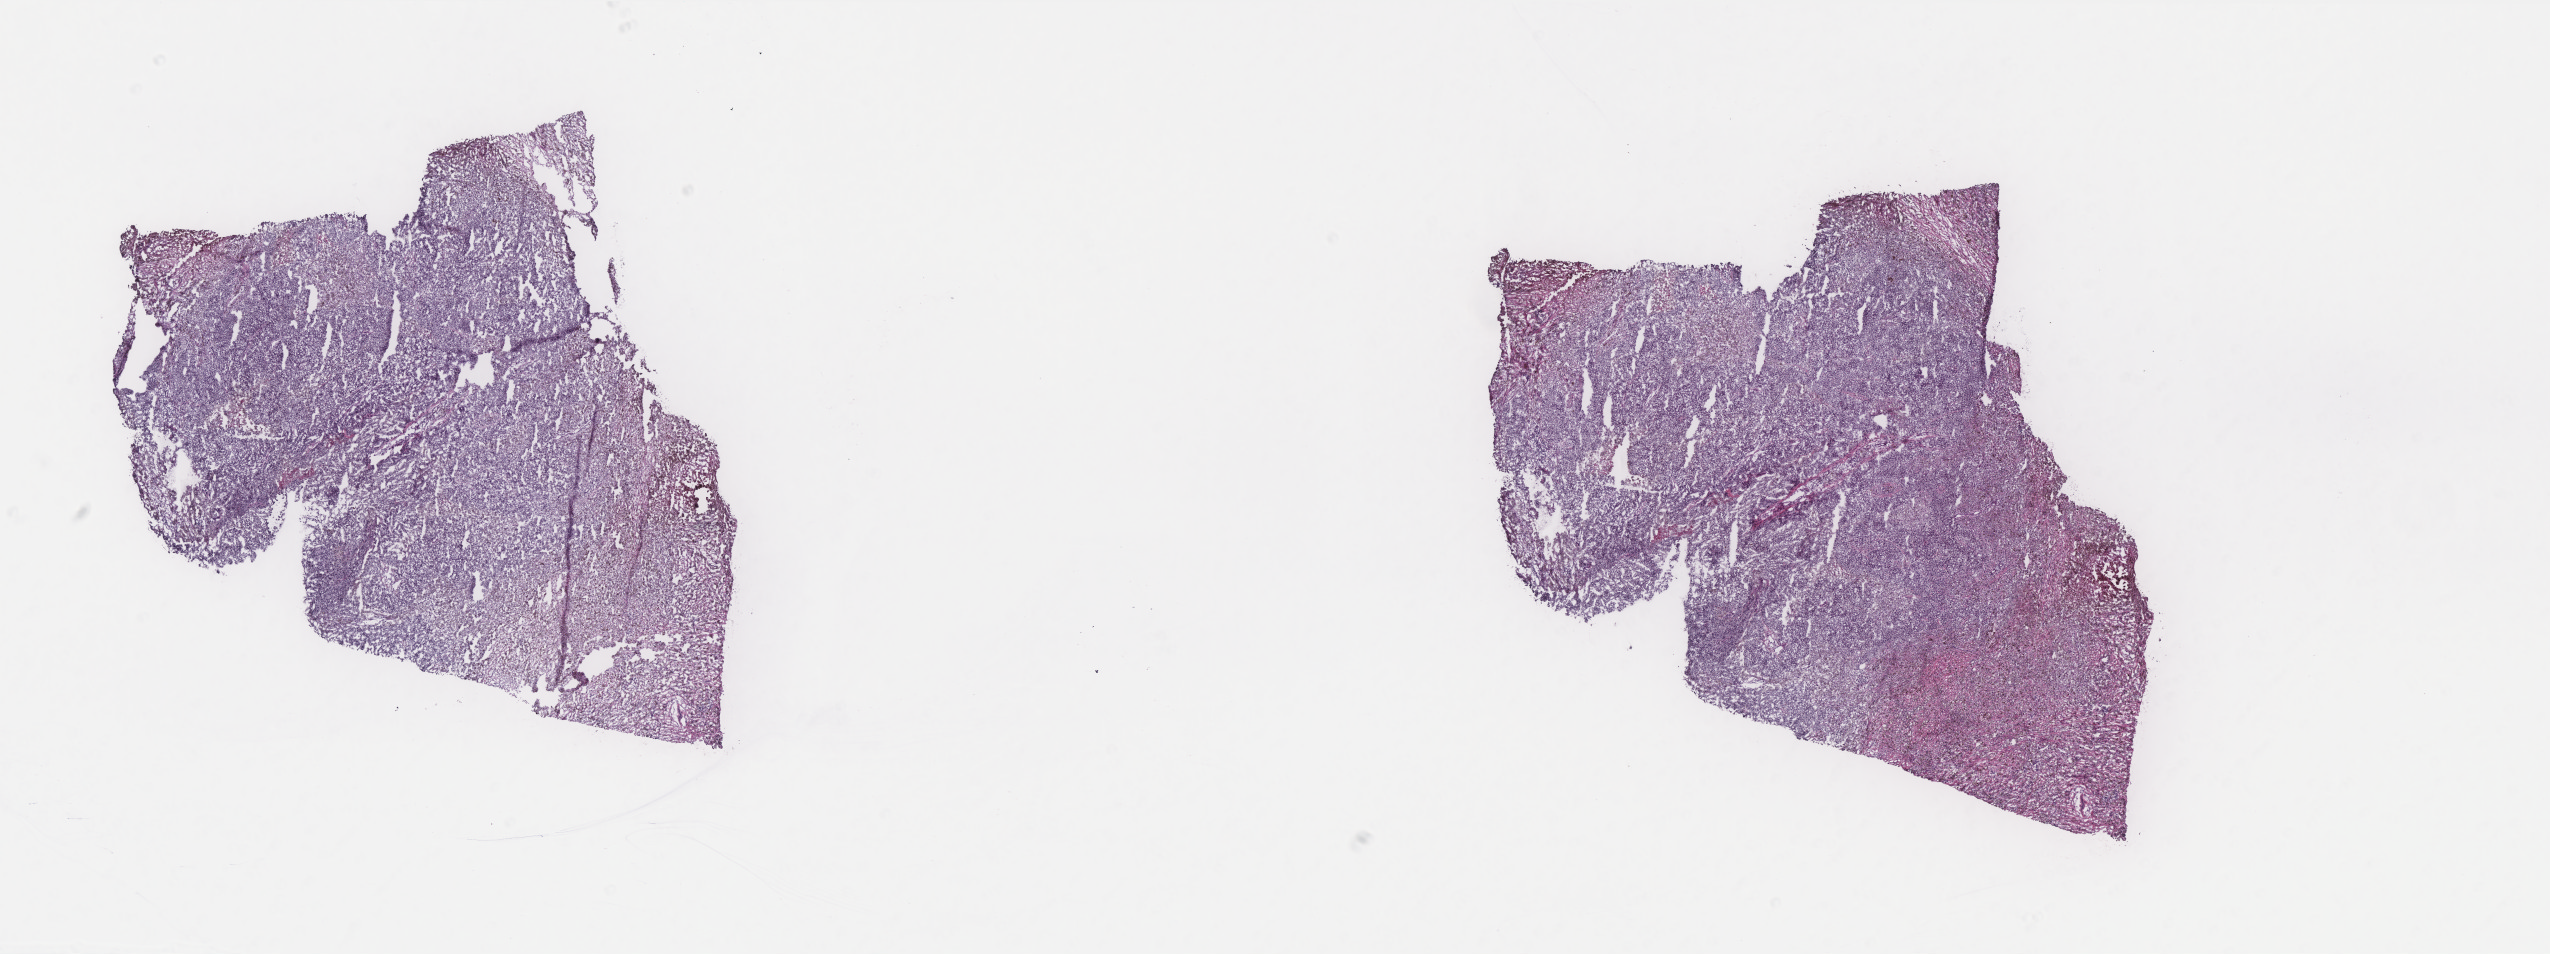
Digitized H&E-stained tissue section (whole slide) — shown as a low-resolution overview of the whole scanned area (about 20.4 x 7.6 mm, from a 40x scan). Frozen section from the top of the tissue portion. Metastatic tumour sample, sampled site not recorded. Male patient; age at initial diagnosis 56 years. Pathologist review of this section (percent, as recorded): tumour cells 75%, tumour nuclei 65%, normal cells 0%, stromal cells 25%, necrosis 0%. Infiltration values recorded for this section: lymphocyte infiltration 0%, monocyte infiltration 0%, neutrophil infiltration 0%.
This section: metastatic tumour tissue. Patient diagnosis: Malignant melanoma, NOS.